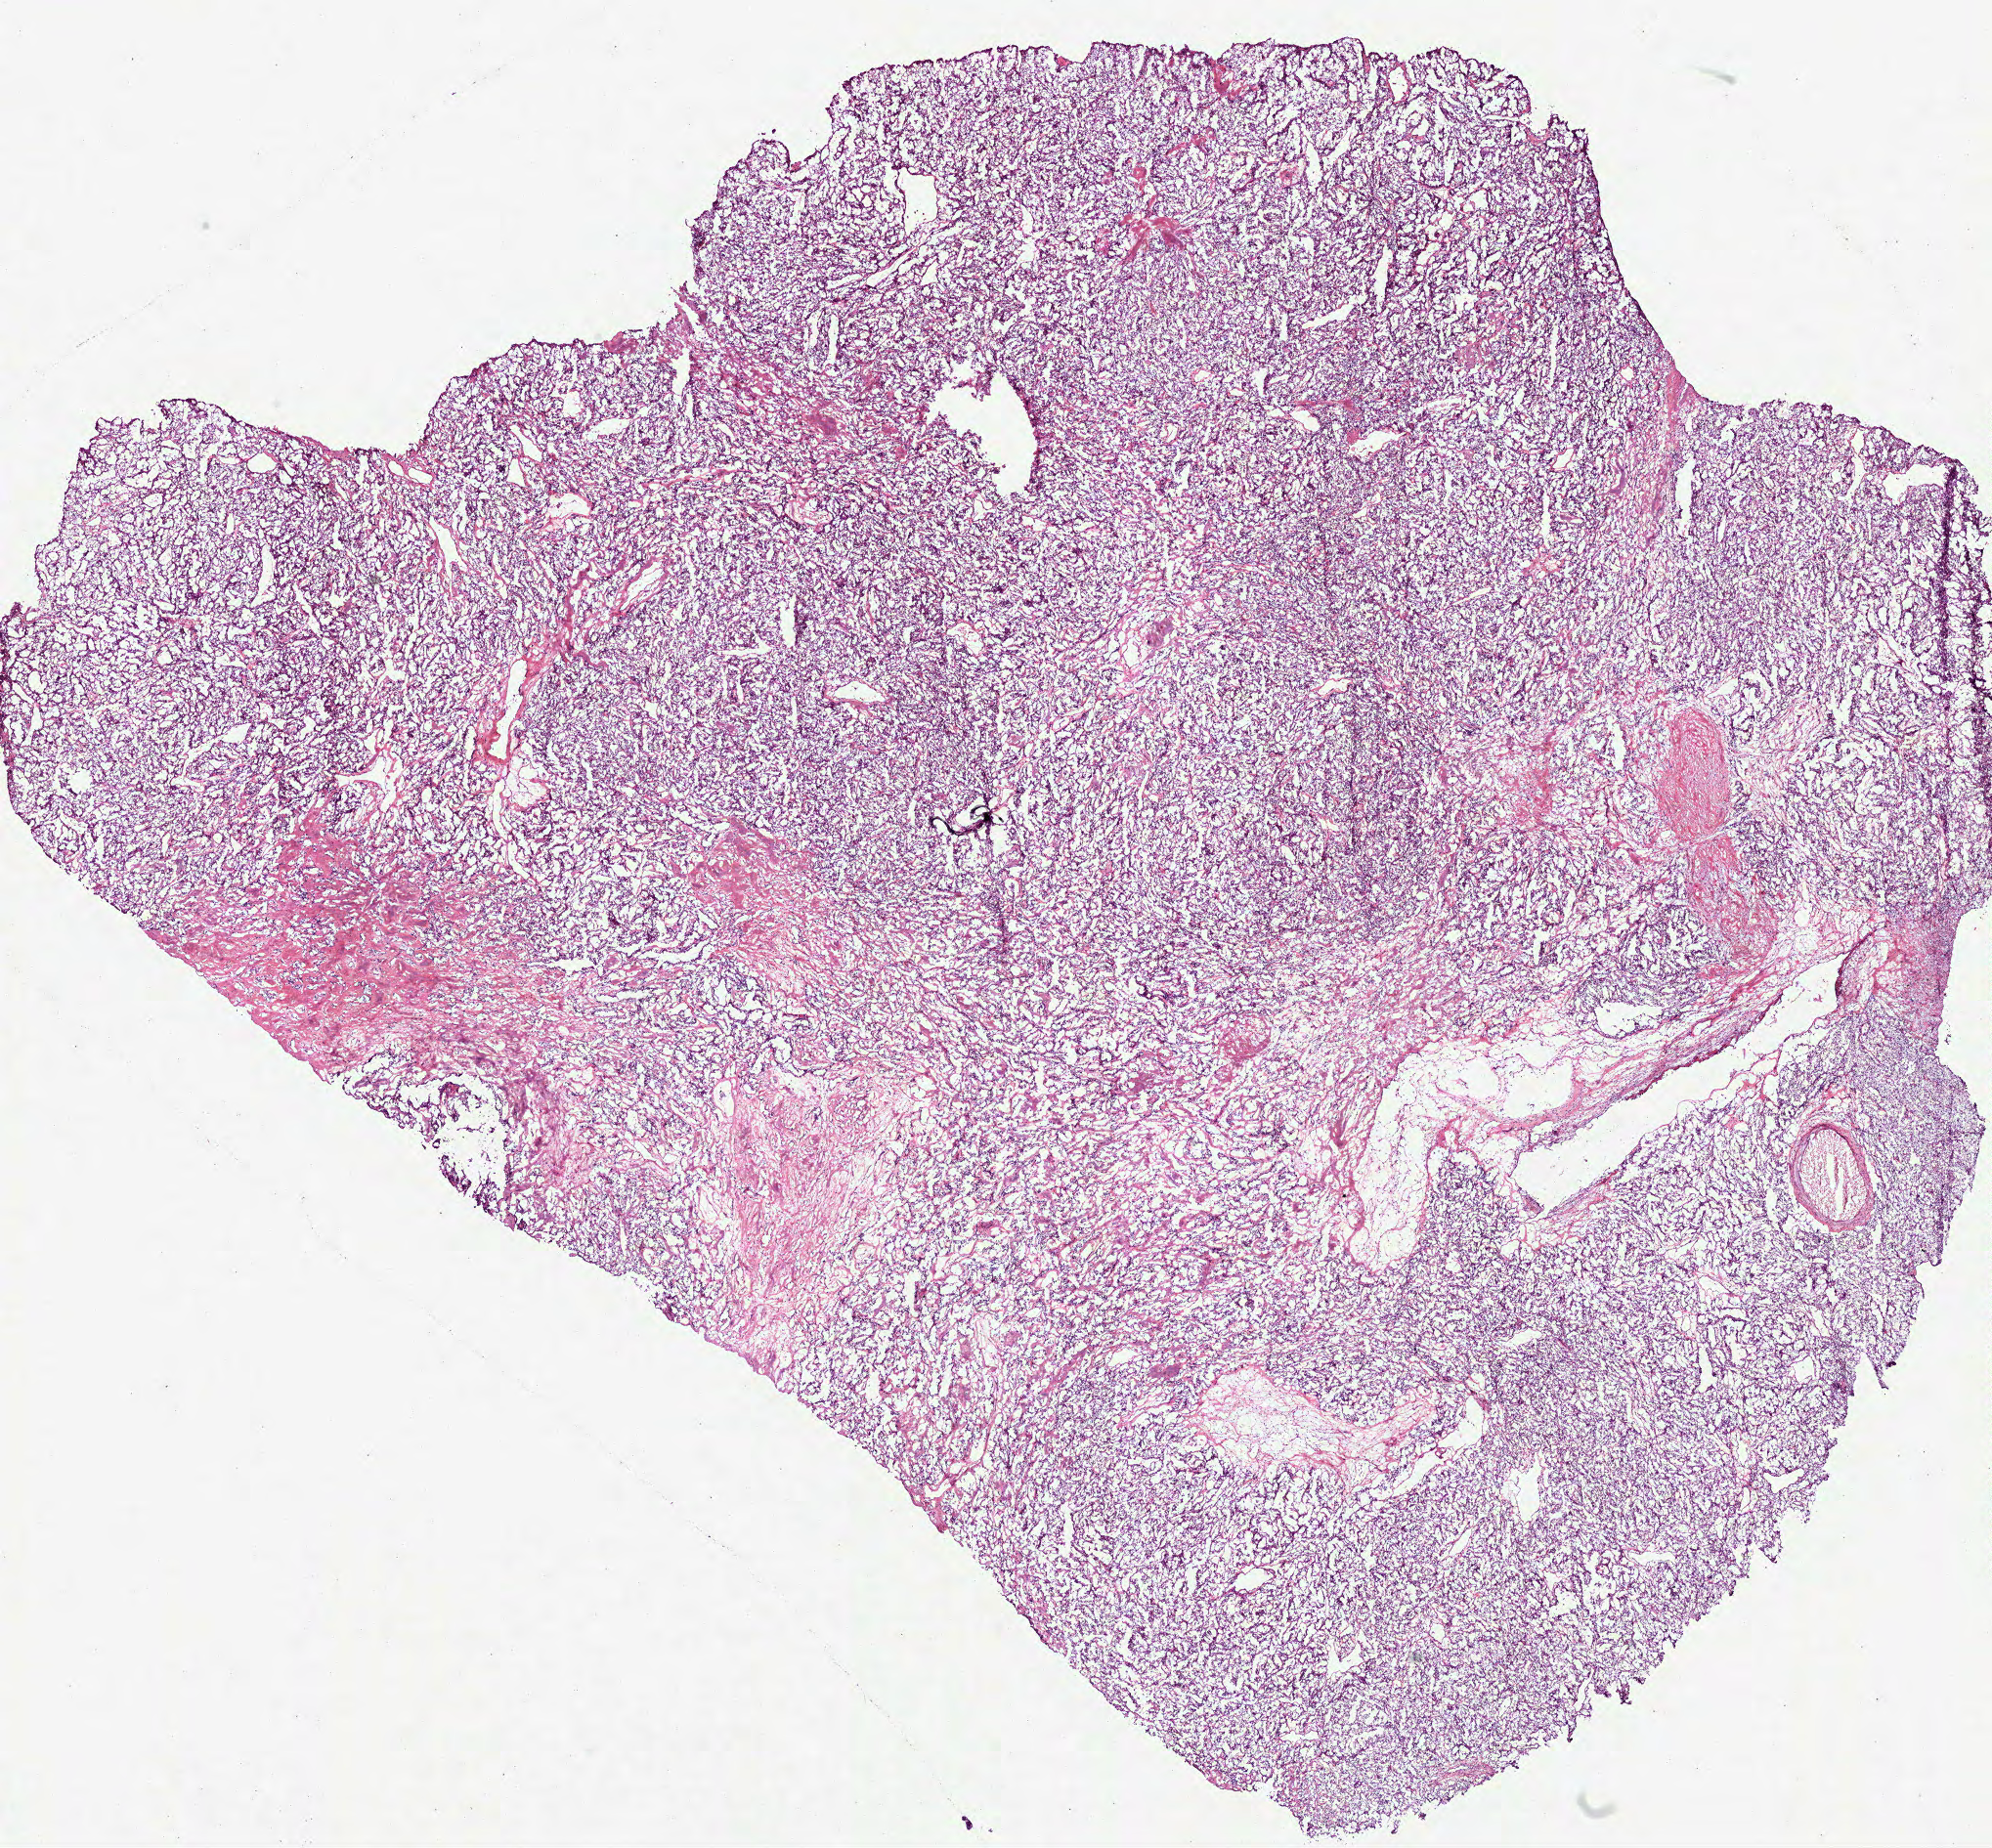
Whole-slide histology image, Hematoxylin and eosin (H&E) stained — a low-resolution overview of the entire scanned area, about 16.4 x 15.3 mm; frozen section; sample: primary tumour, kidney. Male, age 51 years at initial diagnosis. Histologic grade: G3 (poorly differentiated). Composition of this section per pathologist review: tumour cells 85%, tumour nuclei 80%, normal cells 0%, stromal cells 15%, necrosis 0%.
Laterality: left. Diagnosis: Clear cell adenocarcinoma, NOS. AJCC pathologic stage: I (6th edition).